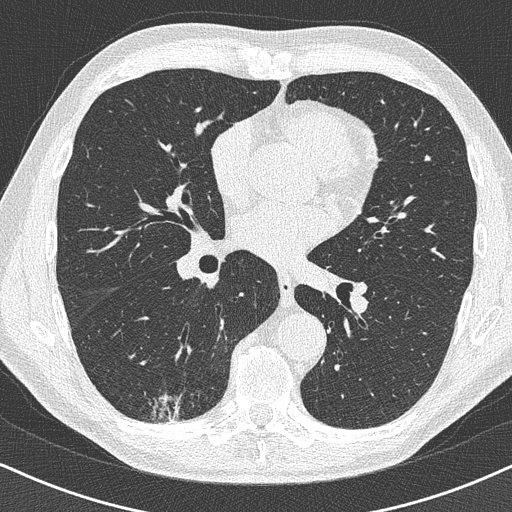
Low-dose screening chest CT, axial slice, first (baseline) screen, lung window (W 1500 / L -600 HU), 1 mm slice thickness, lung (sharp) reconstruction kernel (B50f), slice 222 of 438 in the series, 512 × 512 image matrix, field of view 320 × 320 mm. Male participant, aged 63 years at enrolment. Former smoker at enrolment.
Expert-annotated lung lesion, bounding box <130,361,202,428> (left, top, right, bottom; pixels). Screening reader's record for this exam (one nodule recorded; not confirmed to be the boxed lesion): non-calcified nodule or mass ≥4 mm, right lower lobe, 16 × 13 mm, poorly defined margins. Official screen result: positive, change unspecified: nodule(s) >= 4 mm or enlarging nodule(s), mass(es), or other non-specific abnormalities suspicious for lung cancer. Lung cancer was diagnosed 74 days after this screen: adenocarcinoma, NOS, right lower lobe, moderately differentiated (G2), stage IA (AJCC 6th edition), 20 mm at pathology.